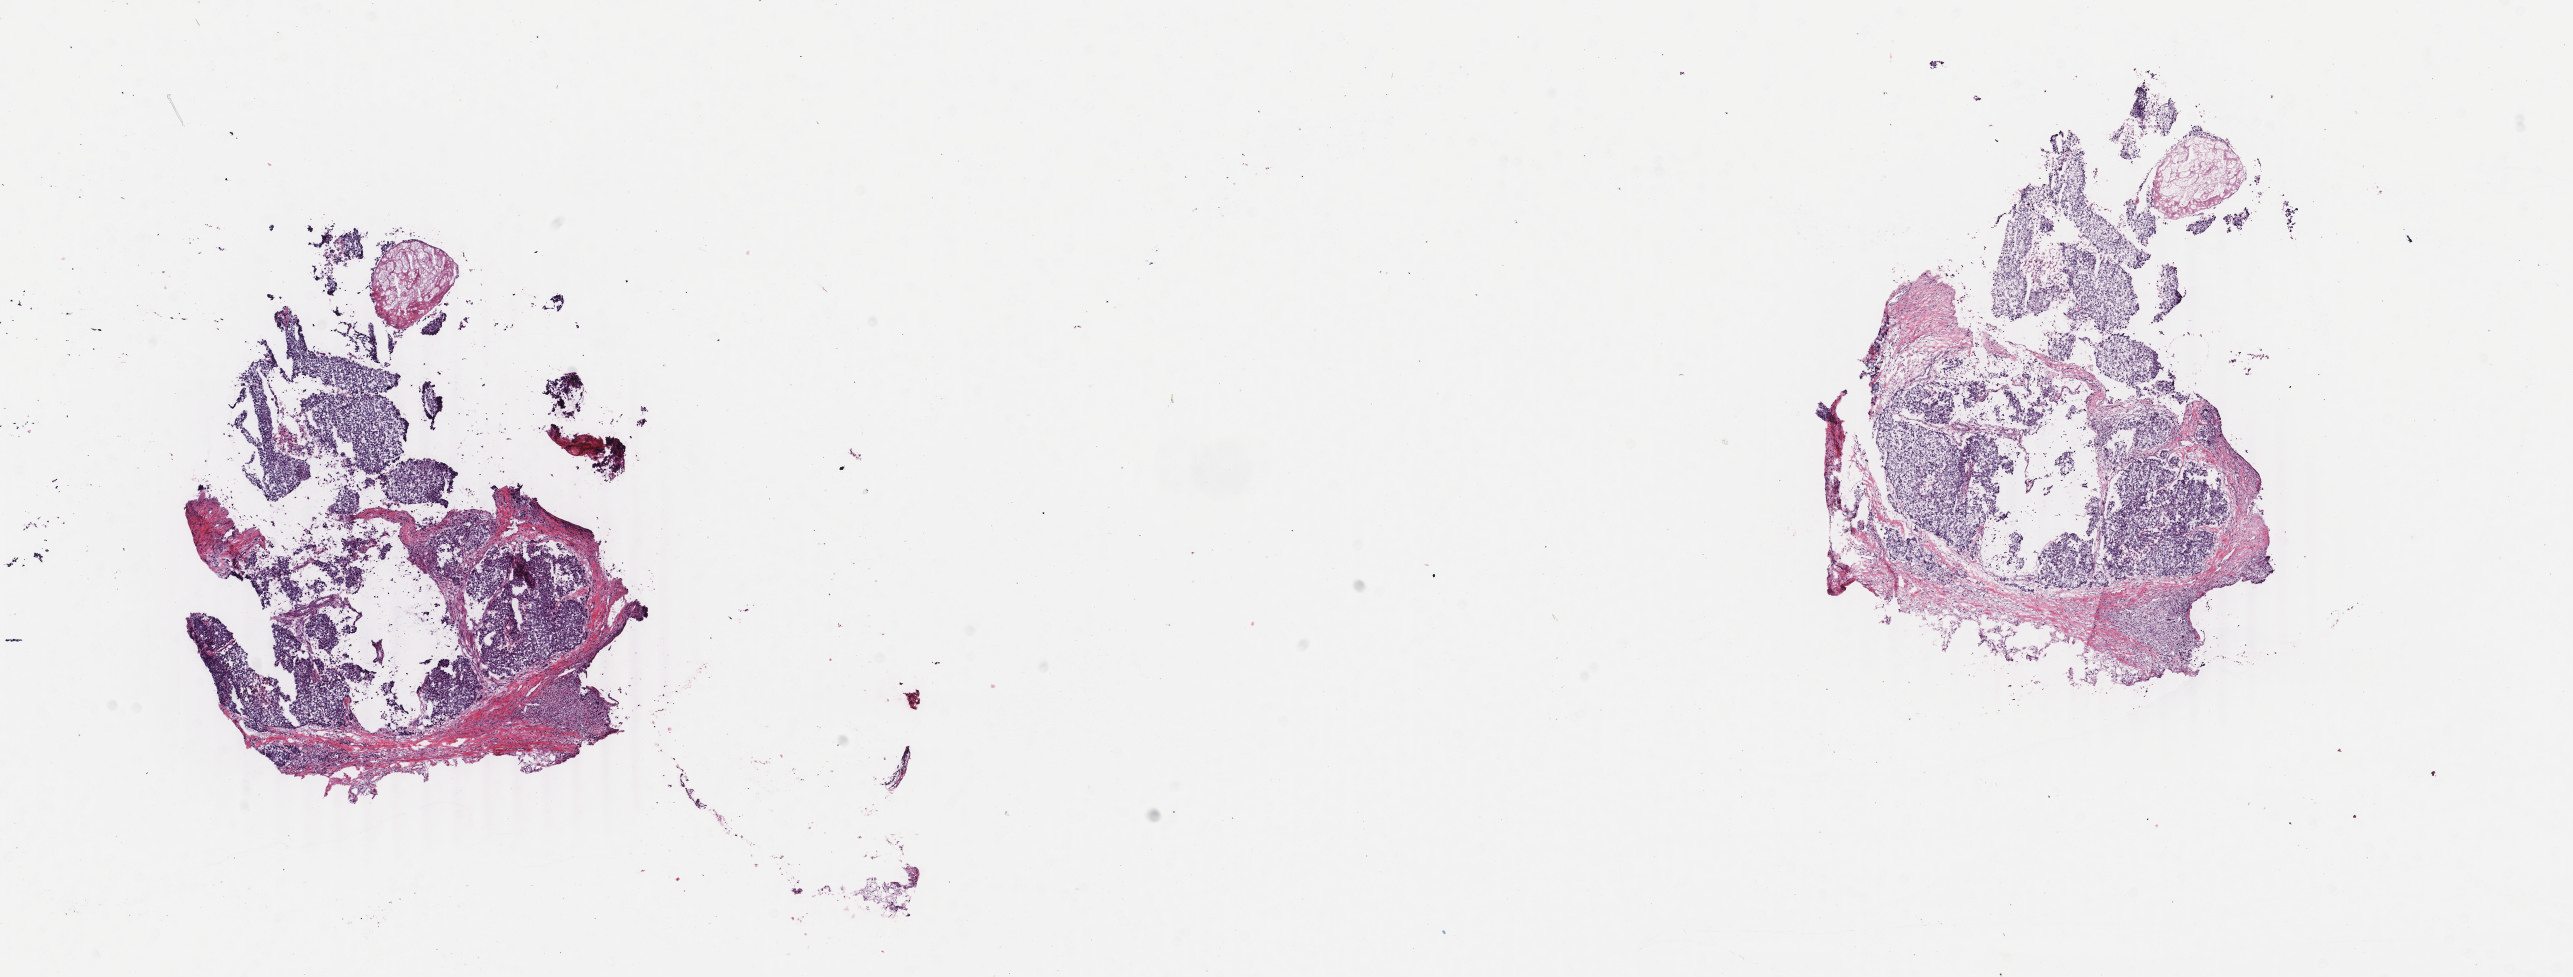
Whole-slide histology image, H&E-stained, a low-resolution overview of the entire scanned area, about 20.5 x 7.8 mm; frozen section from the bottom of the tissue portion; sample: primary tumour, breast. Female patient; age at initial diagnosis 36 years. Slide review estimates, as recorded: tumour cells 80%, tumour nuclei 80%, normal cells 0%, stromal cells 18%, necrosis 2%. Infiltration values recorded for this section: lymphocyte infiltration 1%, monocyte infiltration 1%, neutrophil infiltration 0%.
TNM: T2 N0 (i-) M0. Histologic diagnosis: Infiltrating duct carcinoma, NOS. Lymph nodes positive (case pathology): 0 of 17 examined. AJCC pathologic stage: IIA (6th edition).